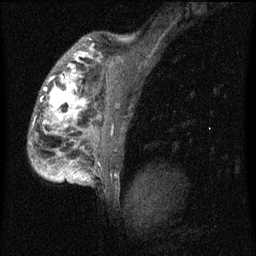
Breast MRI (dynamic contrast-enhanced), one sagittal slice; position 47 of 60 along the scan axis; dynamic contrast-enhanced series, image 2 of 4 at this slice position (ordered by acquisition); 1.5 T; TE 4.2 ms, TR 8 ms; 2 mm slice thickness; 256 × 256 image matrix, field of view 180 × 180 mm. Female patient, age 50 years.
Structures marked on this image (semi-automatically segmented with operator editing):
- analysis volume of interest (the breast-tissue region the enhancement analysis was run in; not a lesion): box from (x=29, y=44) to (x=124, y=177) px
- tumour enhancement mask (voxels above the 70 % enhancement threshold inside the analysis volume of interest): (x=44, y=52)–(x=101, y=175)